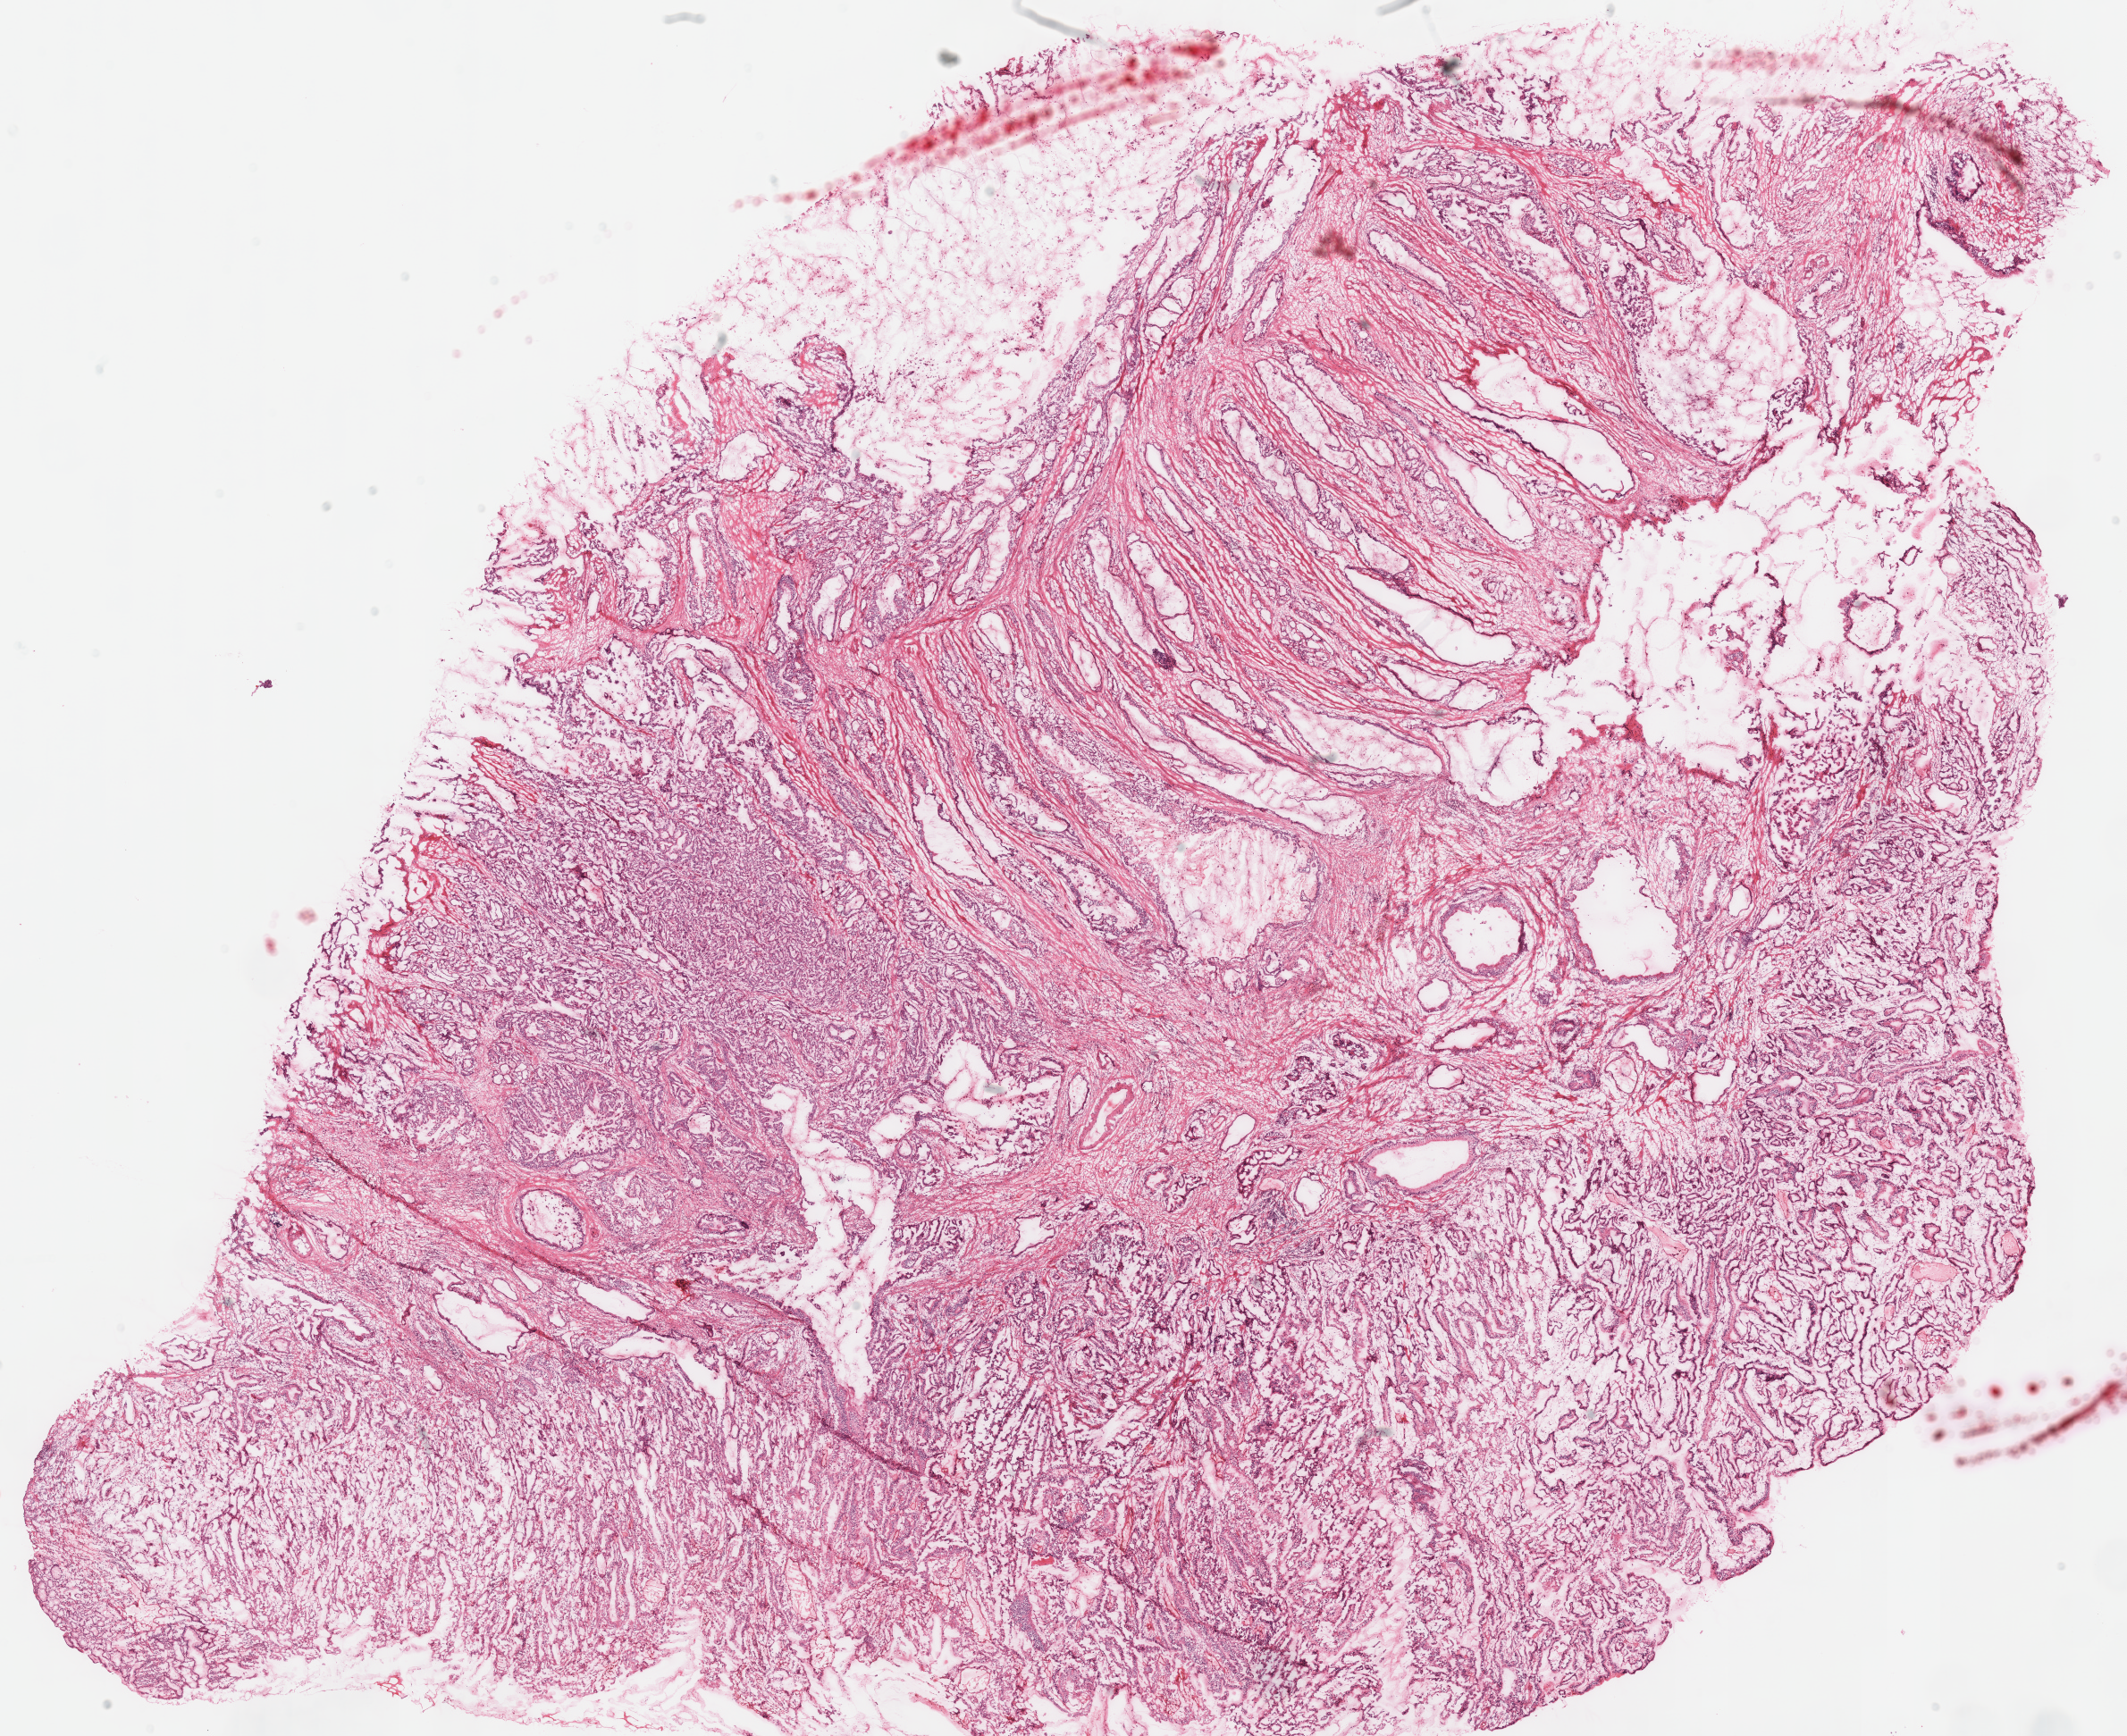
Digitized H&E-stained tissue section (whole slide) — shown as a low-resolution overview of the whole scanned area (about 18.8 x 15.3 mm); frozen section from the top of the tissue portion; stomach, primary tumour sample. Female patient; age at initial diagnosis 67 years. Histologic grade: G3 (poorly differentiated). Slide review estimates, as recorded: tumour cells 90%, tumour nuclei 85%, normal cells 10%, stromal cells 0%, necrosis 0%. Infiltration values recorded for this section: lymphocyte infiltration 5%, monocyte infiltration 5%, neutrophil infiltration 1%.
- AJCC pathologic stage: IIIC (7th edition)
- diagnosis: Adenocarcinoma, NOS (cardia, NOS)
- lymph nodes positive (case pathology): 5 of 9 examined